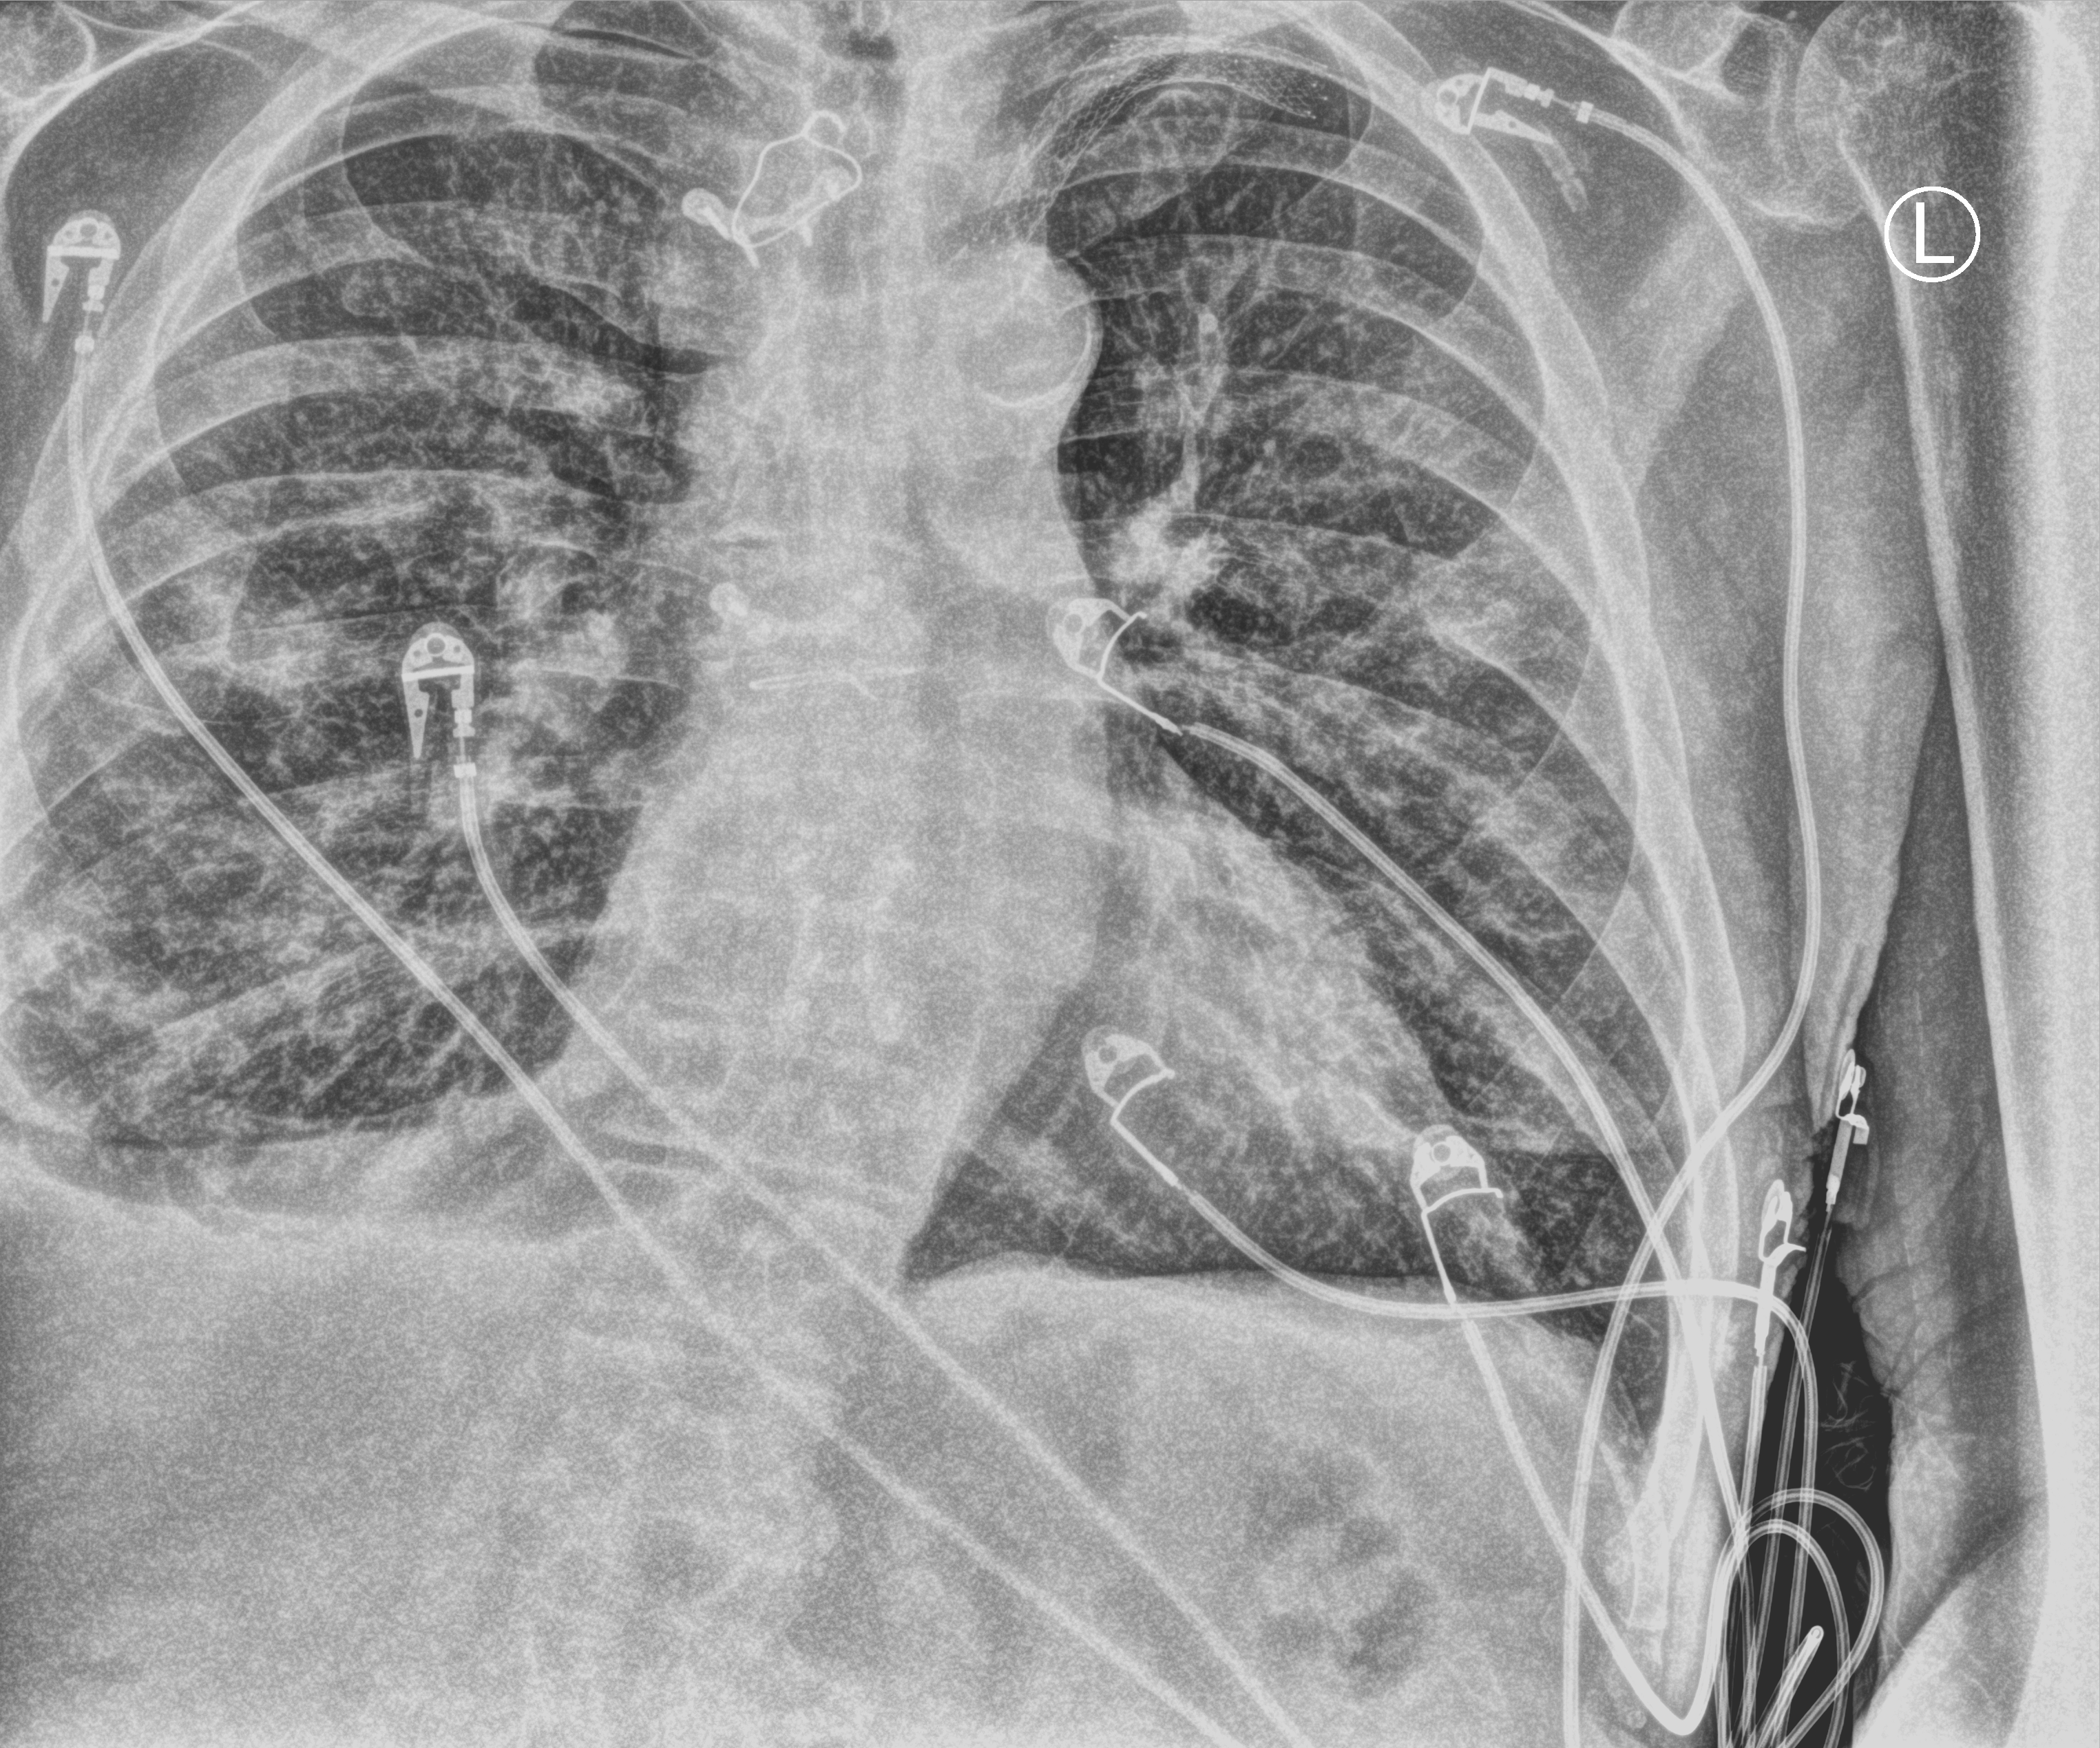
Portable chest radiograph; anteroposterior (AP) projection. Male patient hospitalised with COVID-19, age 75–90 years.
Admission-level facts for this patient (not findings on this image; timing relative to this image not recorded): mechanically ventilated during this hospital stay: no.